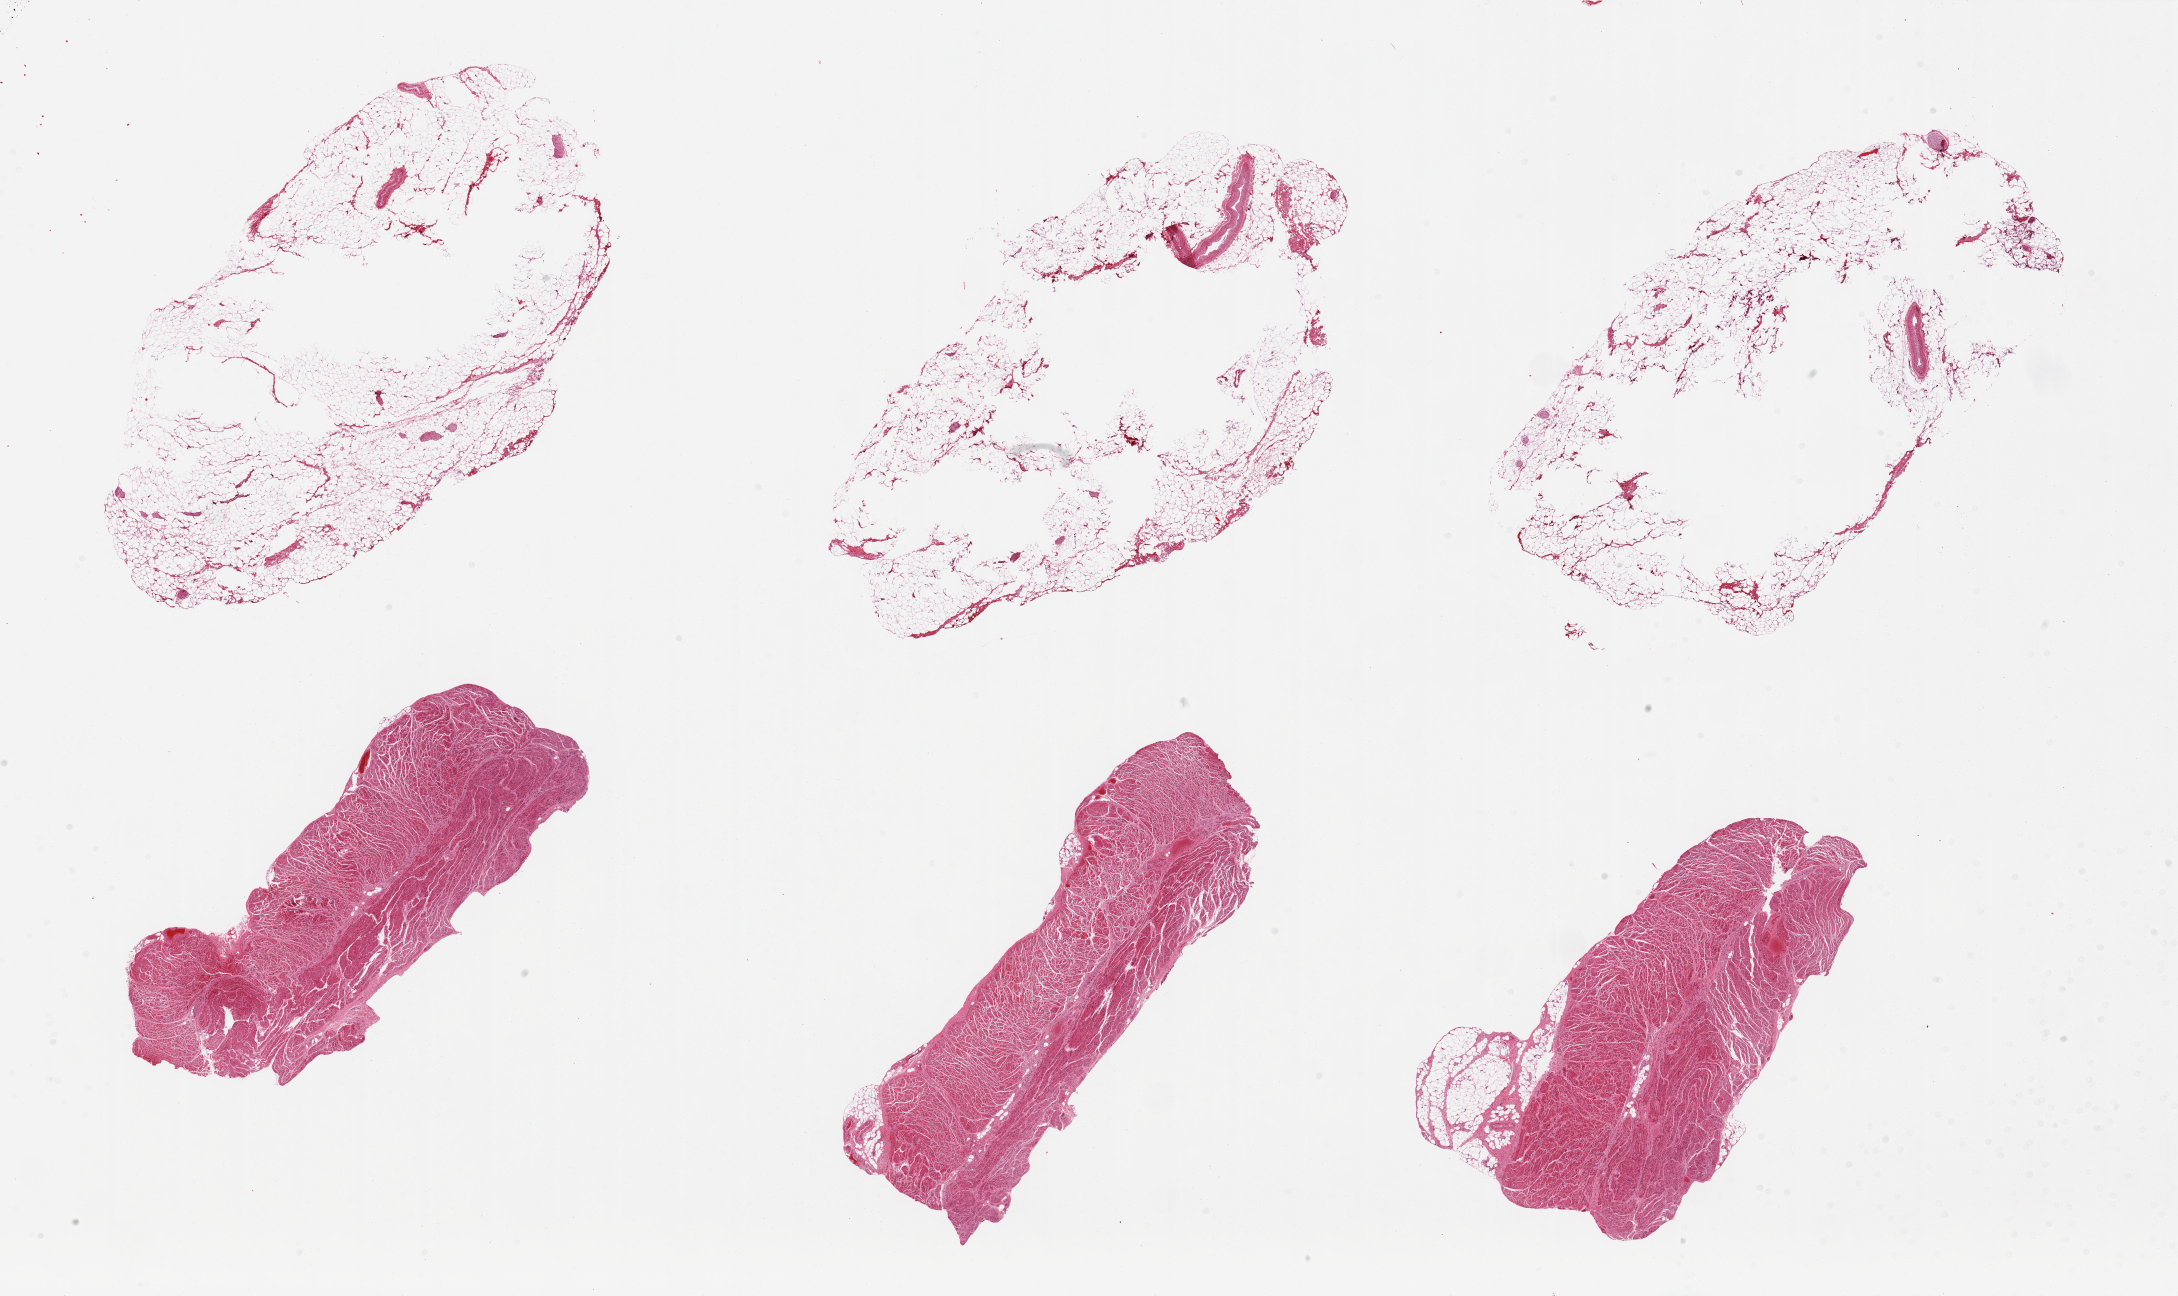
Whole-slide image, haematoxylin and eosin stain, brightfield, shown as a low-resolution overview of the whole scanned area (about 34.5 x 20.5 mm, from a 20x scan). PAXgene-fixed paraffin-embedded (PFPE) section. Sampled site (target tissue): gastroesophageal junction. Donor tissue sample. Donor sex: male.
Pathologist's review note for this sample: 6 pieces, 3 are fat with central defects, 3 are muscularis.